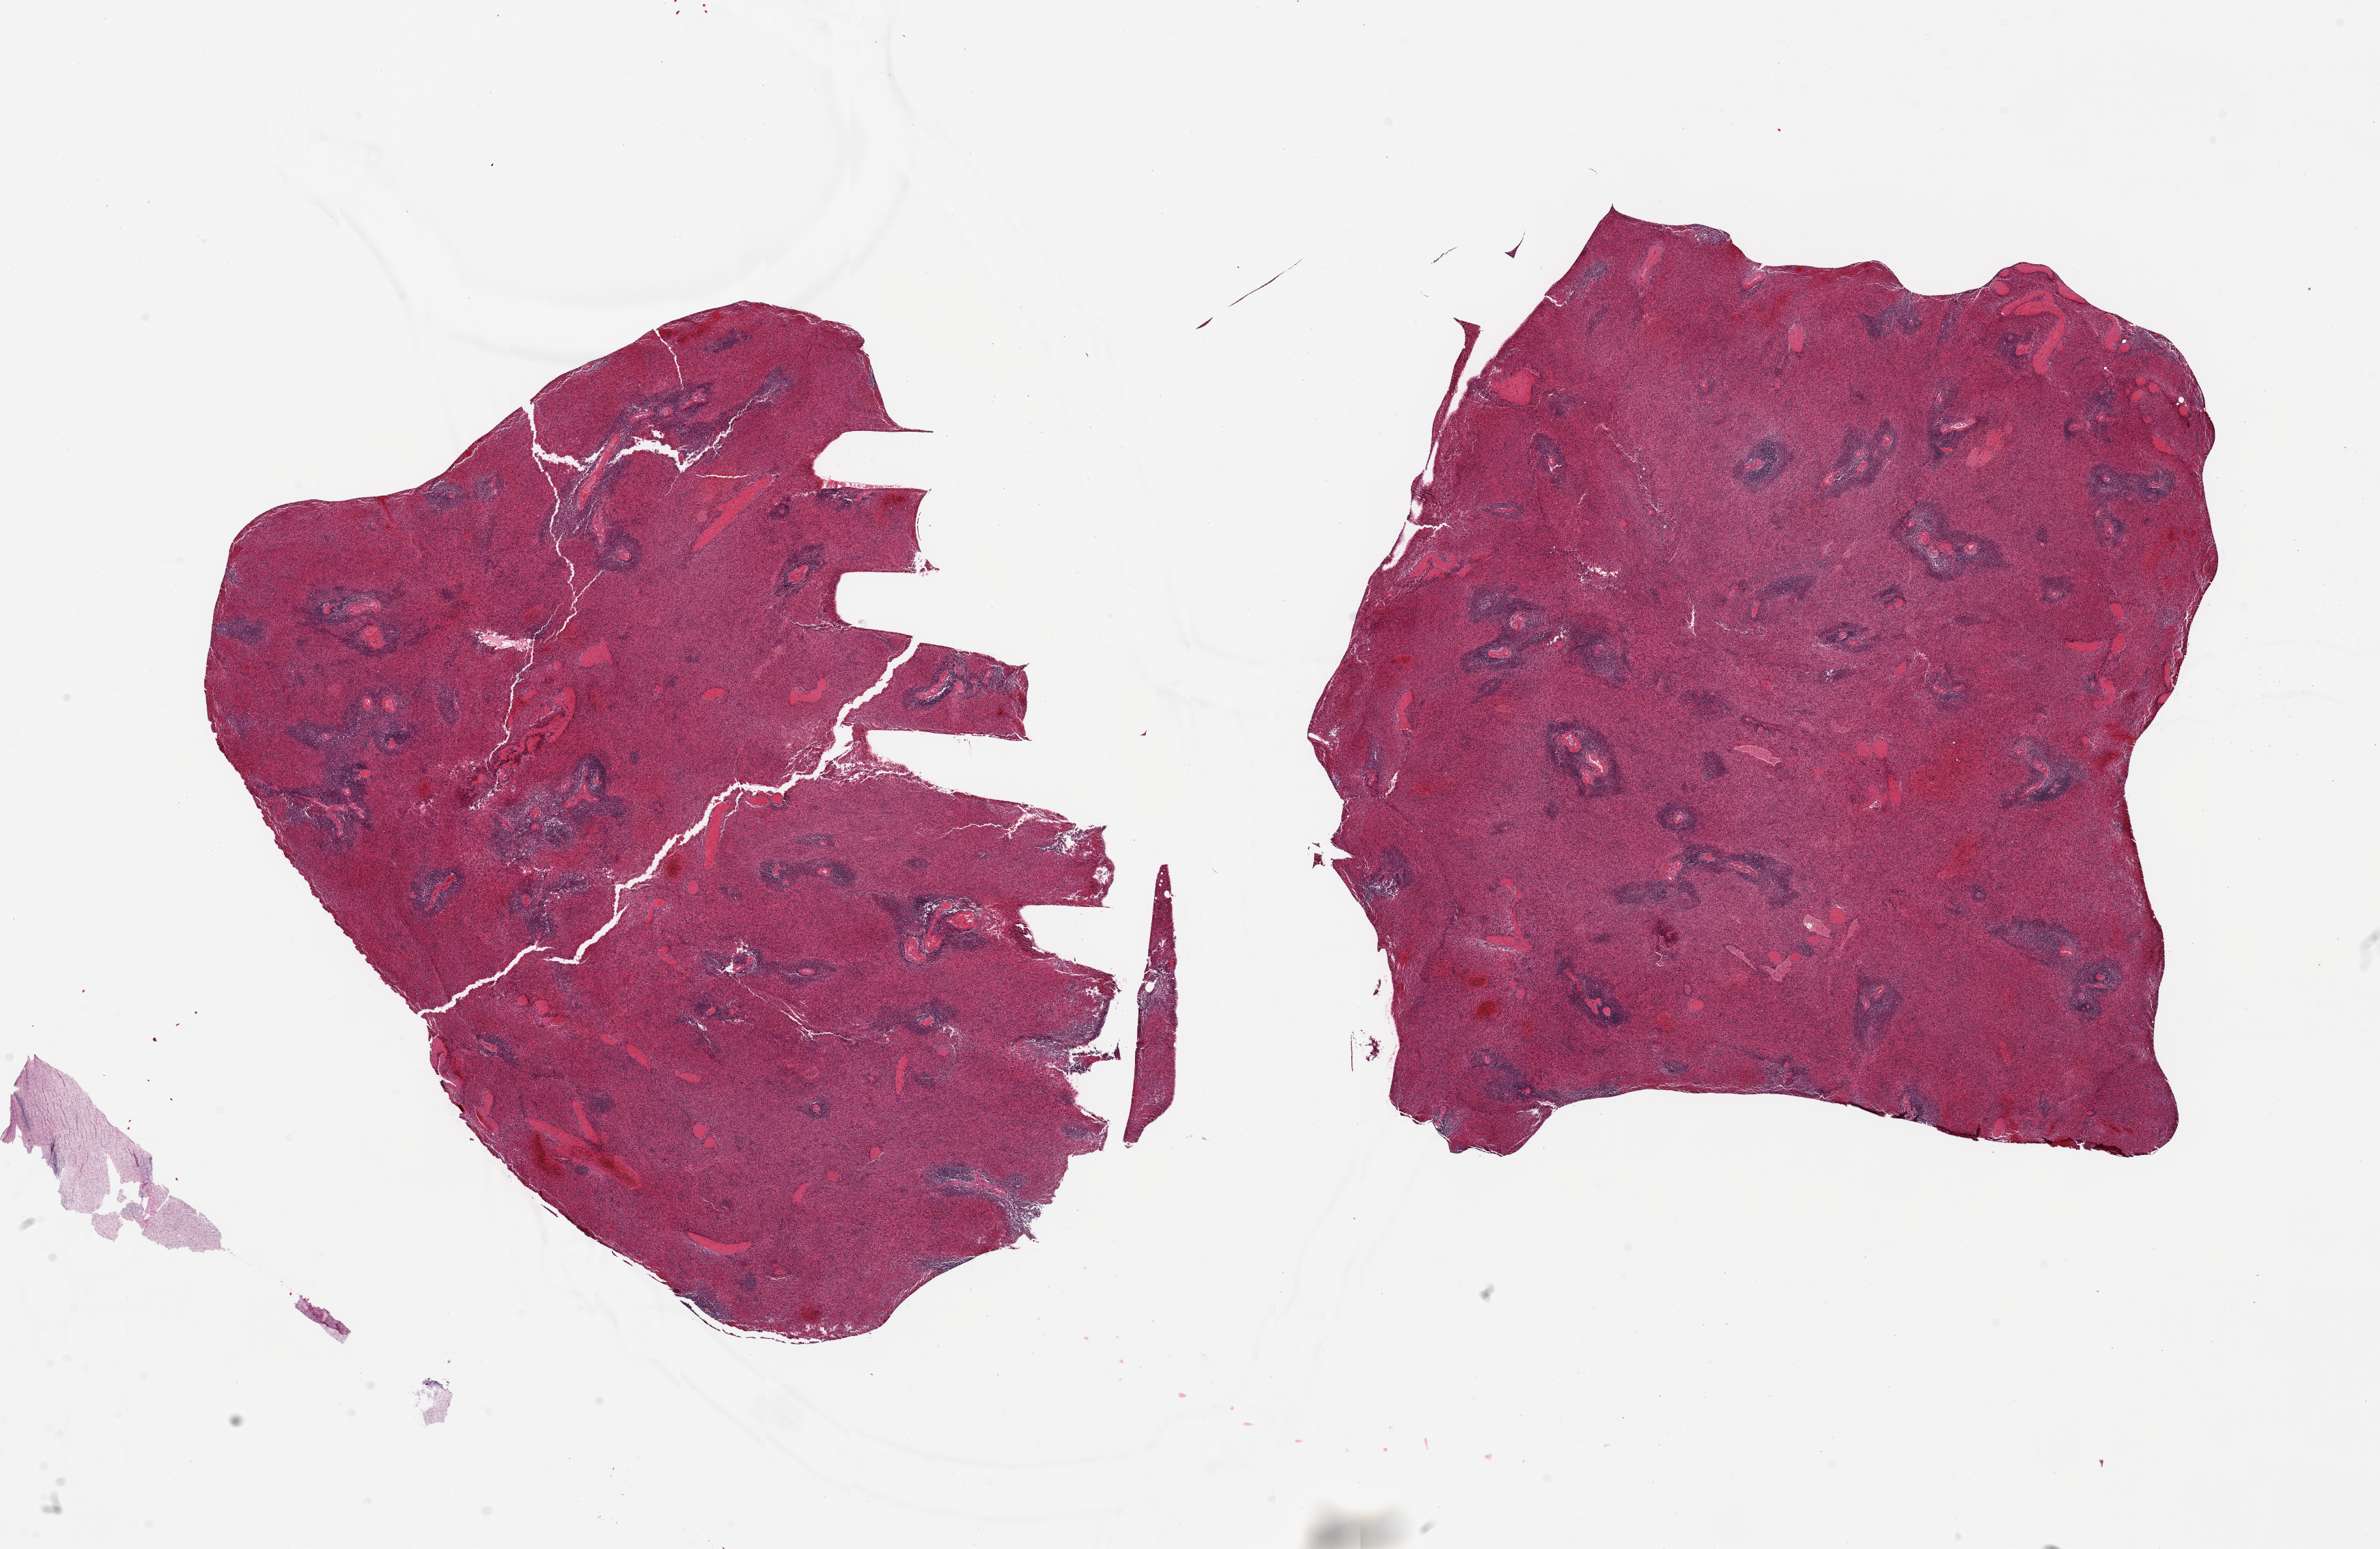
Whole-slide image, haematoxylin and eosin stain — shown as a low-resolution overview of the whole scanned area (about 27.6 x 17.9 mm, acquisition: 20x scan), PAXgene-fixed paraffin-embedded (PFPE) section, sampled site (target tissue): spleen, donor tissue sample.
Pathologist's review note for this sample: 2 pieces mild congestion.